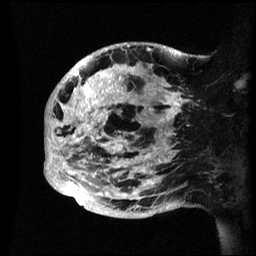
Breast MRI (dynamic contrast-enhanced), one sagittal slice. Slice 19 of 60 in the series (ordered by position). Dynamic contrast-enhanced series, image 2 of 3 at this slice position (ordered by acquisition). 1.5 T. TE 4.2 ms, TR 8.4 ms. 2.4 mm slice thickness. 256 × 256 image matrix. Female patient, age 48 years.
Structures marked on this image (semi-automatic segmentation, software-assisted and operator-edited):
- analysis volume of interest (the breast-tissue region the enhancement analysis was run in; not a lesion): bounding box <44,43,193,218> (left, top, right, bottom; pixels)
- tumour enhancement mask (voxels above the 70 % enhancement threshold inside the analysis volume of interest): <45,44,182,201>